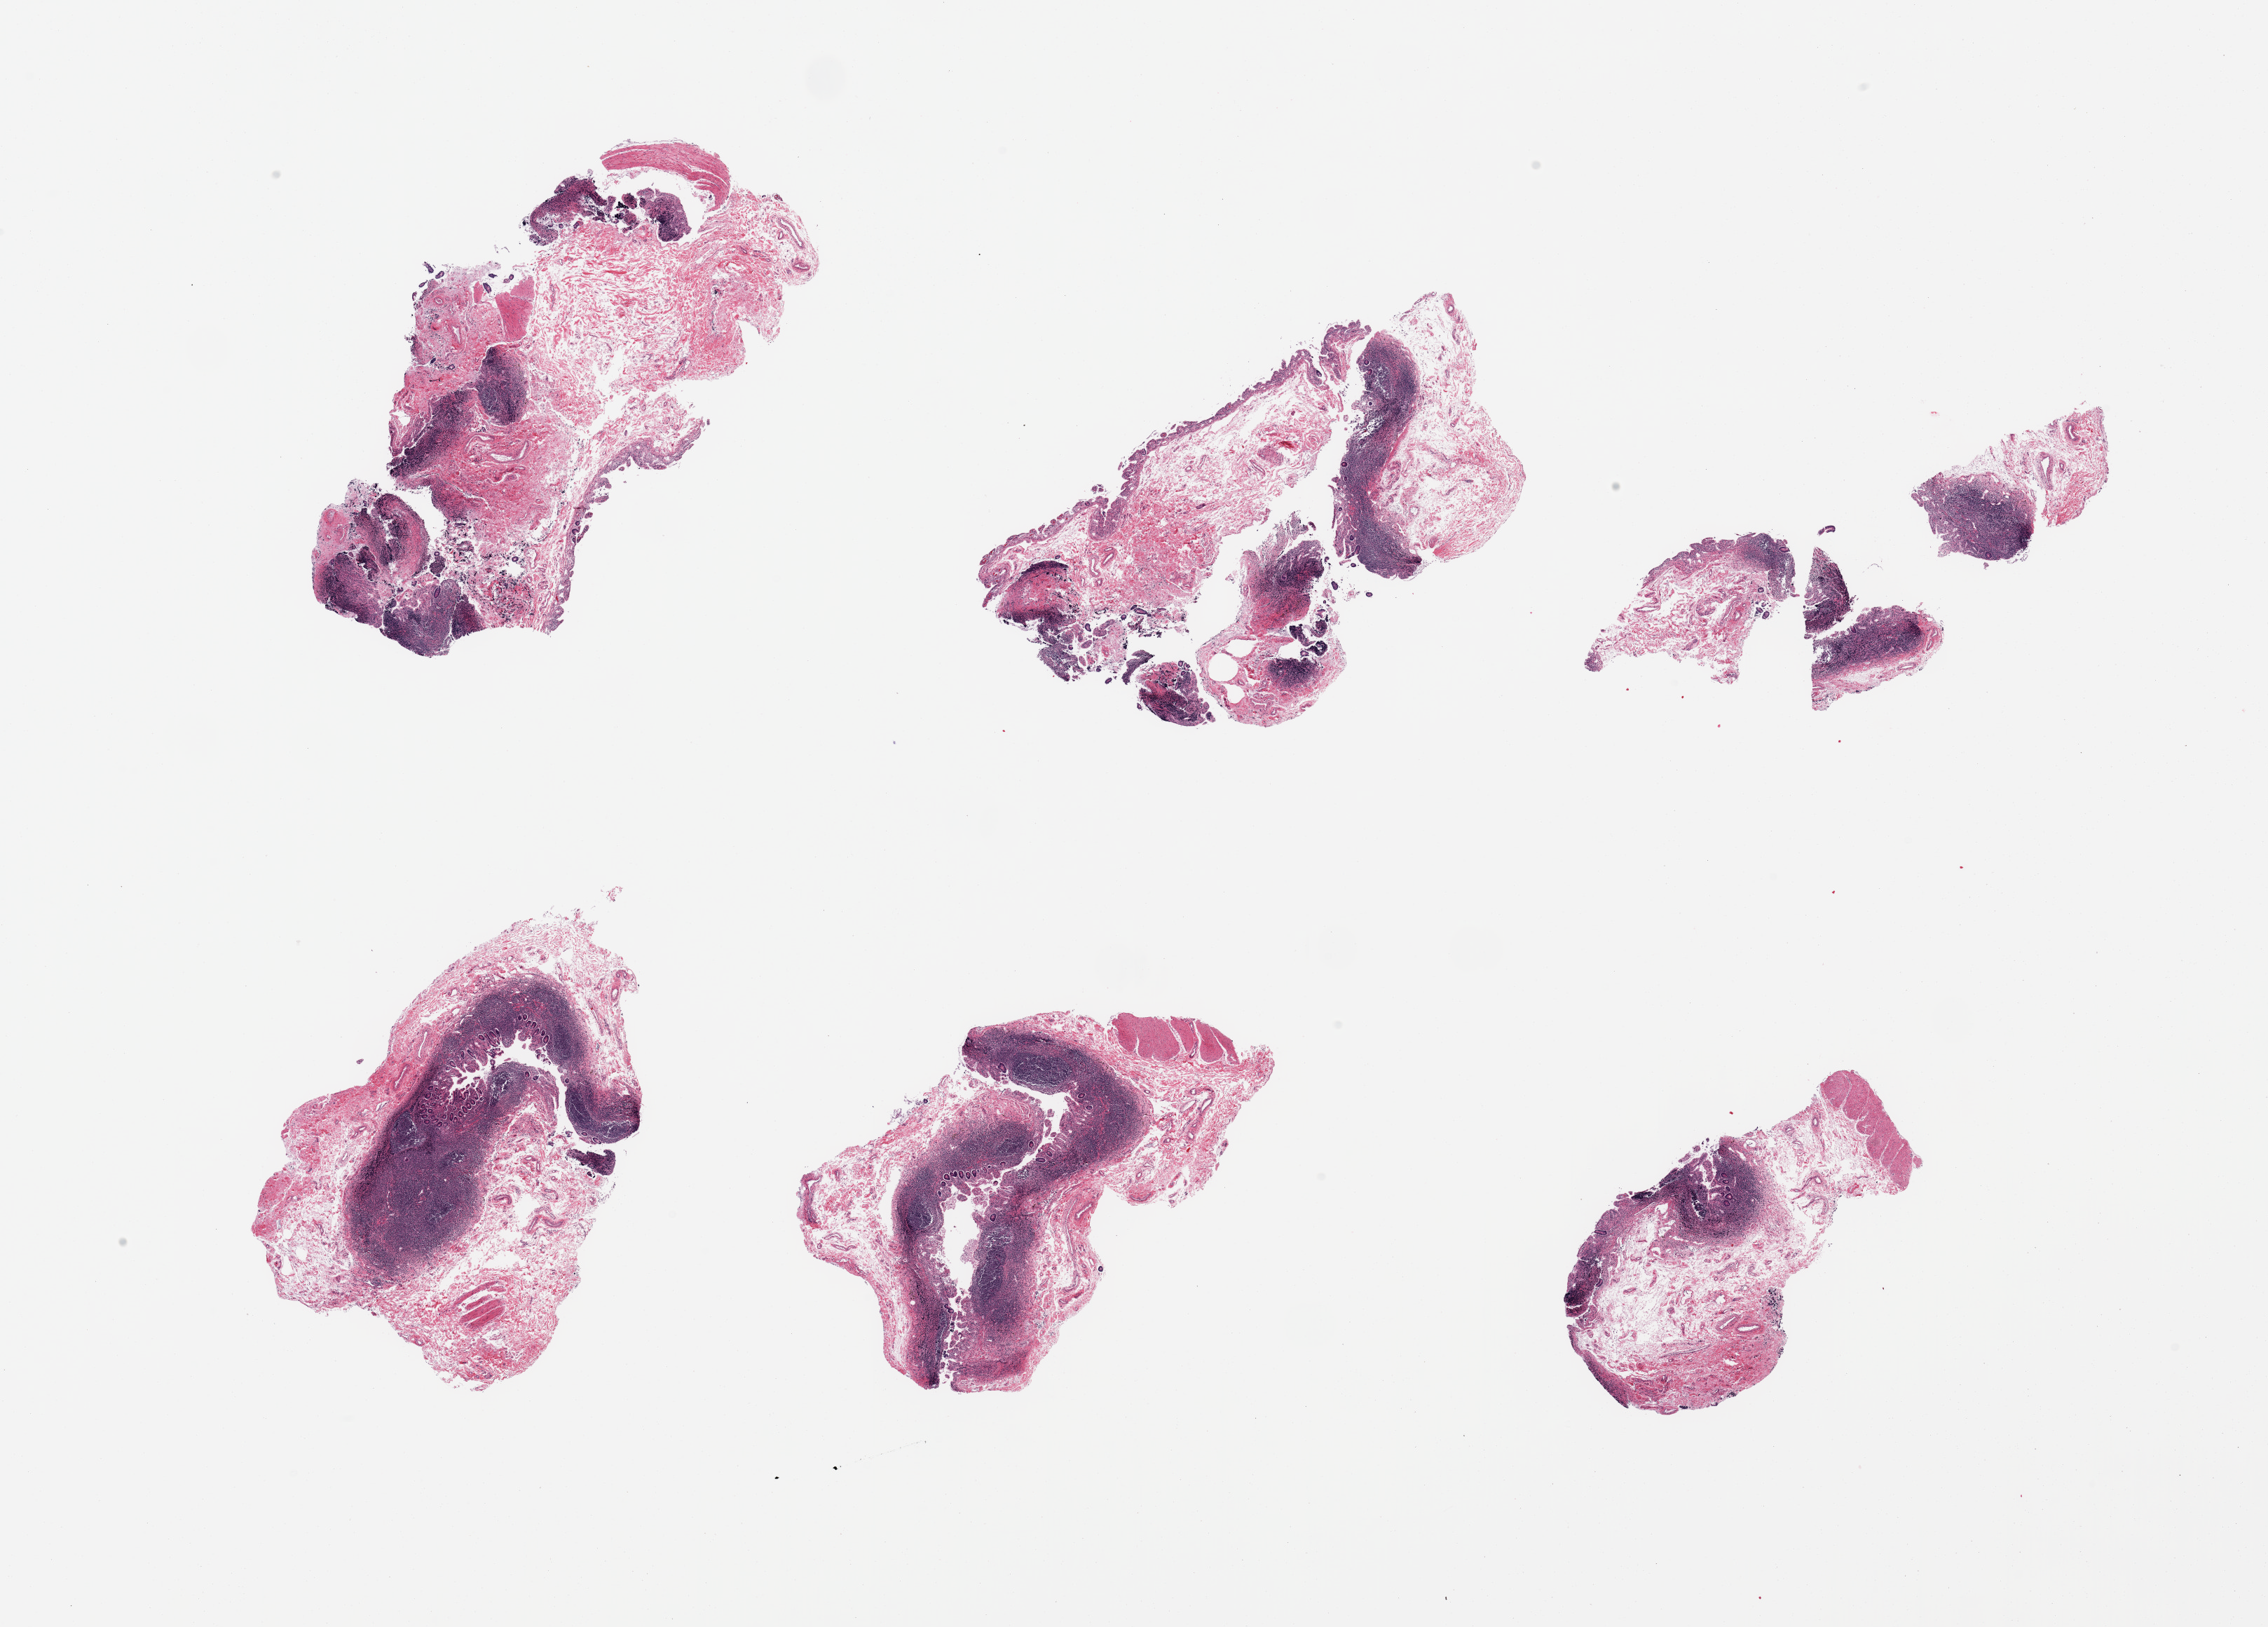
Whole-slide image, hematoxylin and eosin (H&E) stain, whole scanned area (about 25.6 x 18.4 mm) shown as a low-resolution overview, PAXgene-fixed paraffin-embedded (PFPE) section, sampled site (target tissue): ileum, tissue donor sample. Donor: female.
- review note (as recorded): 6 pieces; fragments of mucosa, submucosa, lymphoid aggregates (well represented), and rare portion of muscularis (not target)